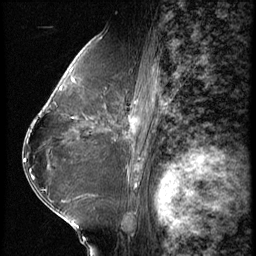
Breast MRI (dynamic contrast-enhanced), one sagittal slice; position 35 of 62 along the scan axis; 3 images stored at this slice position (order not interpretable as contrast timing); 1.5 T; TE 4.2 ms, TR 9 ms; 2.5 mm slice thickness; 256 × 256 image matrix, field of view 180 × 180 mm. Patient: female, 65 years. From the clinical record (not read from this slice): setting: breast cancer imaged before/during neoadjuvant chemotherapy; receptor status: HR-positive, HER2-negative.
Structures marked on this image (semi-automatically segmented with operator editing):
- analysis volume of interest (the breast-tissue region the enhancement analysis was run in; not a lesion): bounding box [x1, y1, x2, y2] px = [104, 104, 154, 161]
- tumour enhancement mask (voxels above the 140 % enhancement threshold inside the analysis volume of interest): [130, 105, 154, 161]